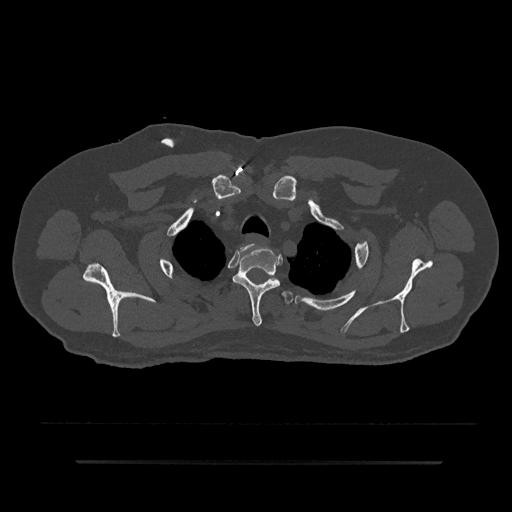
CT including the spine, one axial slice; position 694 of 797 along the scan axis; reconstruction kernel Br40s/3; 120 kVp; bone window (W 1800 / L 400 HU); 0.5 mm slice thickness; 512 × 512 image matrix, field of view 464 × 464 mm. Male patient, age 59 years. From the clinical record (not read from this slice): primary cancer: bile ducts; vertebrae with lytic lesions (as recorded): T10.
Structures marked on this image (semi-automatically segmented with operator editing):
- T1 vertebra: bounding box (x1, y1, x2, y2) in pixels: (240, 245, 267, 252)
- T2 vertebra: (233, 247, 281, 326)
- T3 vertebra: (282, 291, 293, 304)